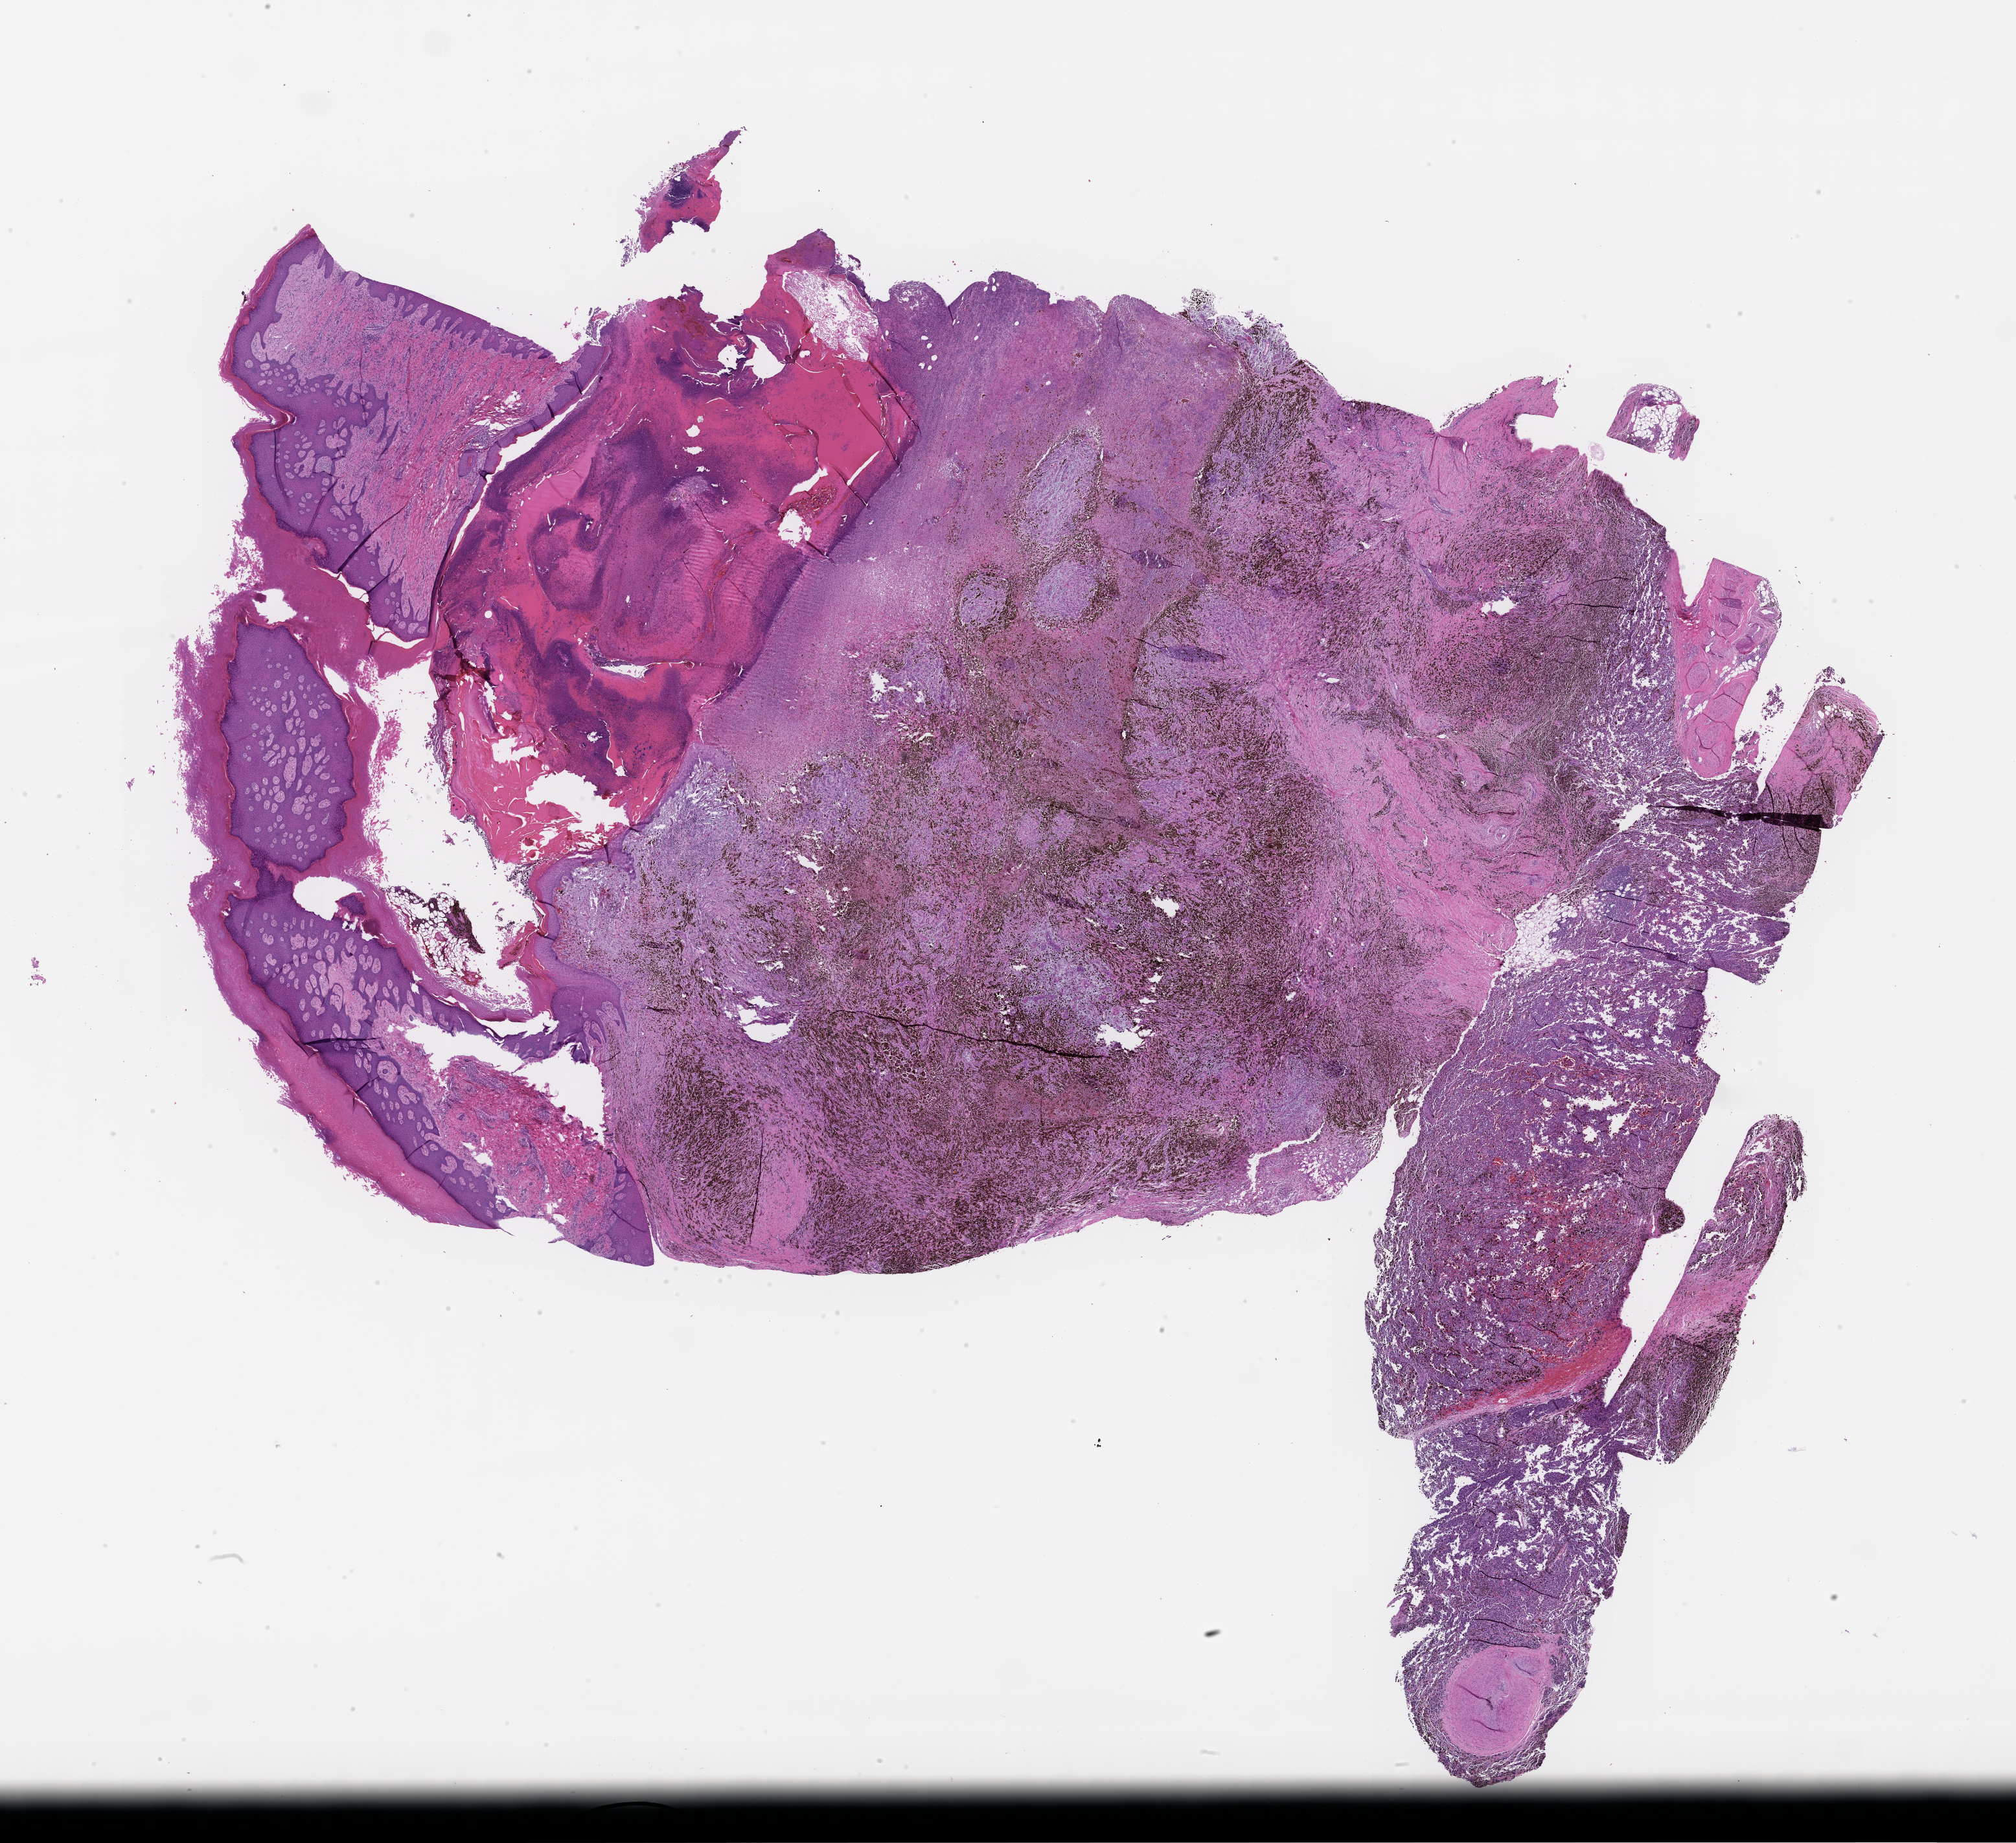
Haematoxylin and eosin whole-slide image — shown as a low-resolution overview of the whole scanned area (about 25.1 x 23.0 mm), formalin-fixed, paraffin-embedded (FFPE) tissue, tissue site: skin. Patient sex: male.
This section: primary tumor. Diagnosis: Melanoma.